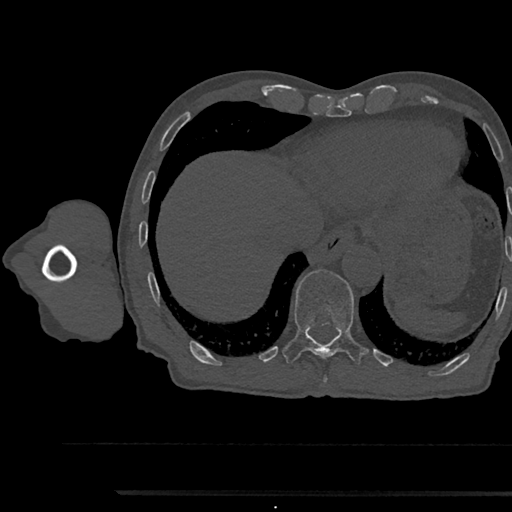
CT including the spine, one axial slice. Slice 794 of 797 in the series (ordered by position). Reconstruction kernel Br40s/3. 120 kVp. Bone window (W 1800 / L 400 HU). 512 × 512 image matrix, field of view 367 × 367 mm. Patient: male, 79 years. From the clinical record (not read from this slice): primary cancer: prostate.
Outlined on this slice (semi-automatic segmentation, software-assisted and operator-edited):
- T11 vertebra: bounding box [x1, y1, x2, y2] px = [282, 270, 368, 362]